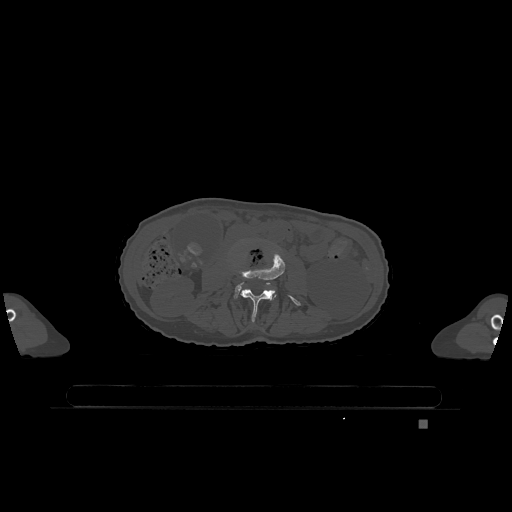
CT including the spine, one axial slice. Slice 345 of 1317 in the series (ordered by position). Bone window (W 1800 / L 400 HU). 512 × 512 image matrix. Female patient, age 74 years. From the clinical record (not read from this slice): primary cancer: lung; vertebrae with lytic lesions (as recorded): T1, T4, T5, T6, L4, L5.
Annotated regions visible in this slice (semi-automatic segmentation, software-assisted and operator-edited):
- L3 vertebra: bounding box <239,251,301,322> (left, top, right, bottom; pixels)
- L4 vertebra: <234,283,273,299>